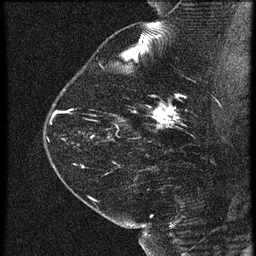
Breast MRI (dynamic contrast-enhanced), one sagittal slice; position 44 of 60 along the scan axis; 3 images stored at this slice position (order not interpretable as contrast timing); 1.5 T; TE 4.2 ms, TR 21.3 ms; 1.5 mm slice thickness; 256 × 256 image matrix, field of view 180 × 180 mm. Patient: female, 42 years. Case-level facts recorded for this patient, not image findings: setting: breast cancer imaged before/during neoadjuvant chemotherapy; receptor status: HER2-positive.
Structures marked on this image (semi-automatic segmentation, software-assisted and operator-edited):
- analysis volume of interest (the breast-tissue region the enhancement analysis was run in; not a lesion): bounding box <122,82,195,147> (left, top, right, bottom; pixels)
- tumour enhancement mask (voxels above the 90 % enhancement threshold inside the analysis volume of interest): <133,94,178,129>